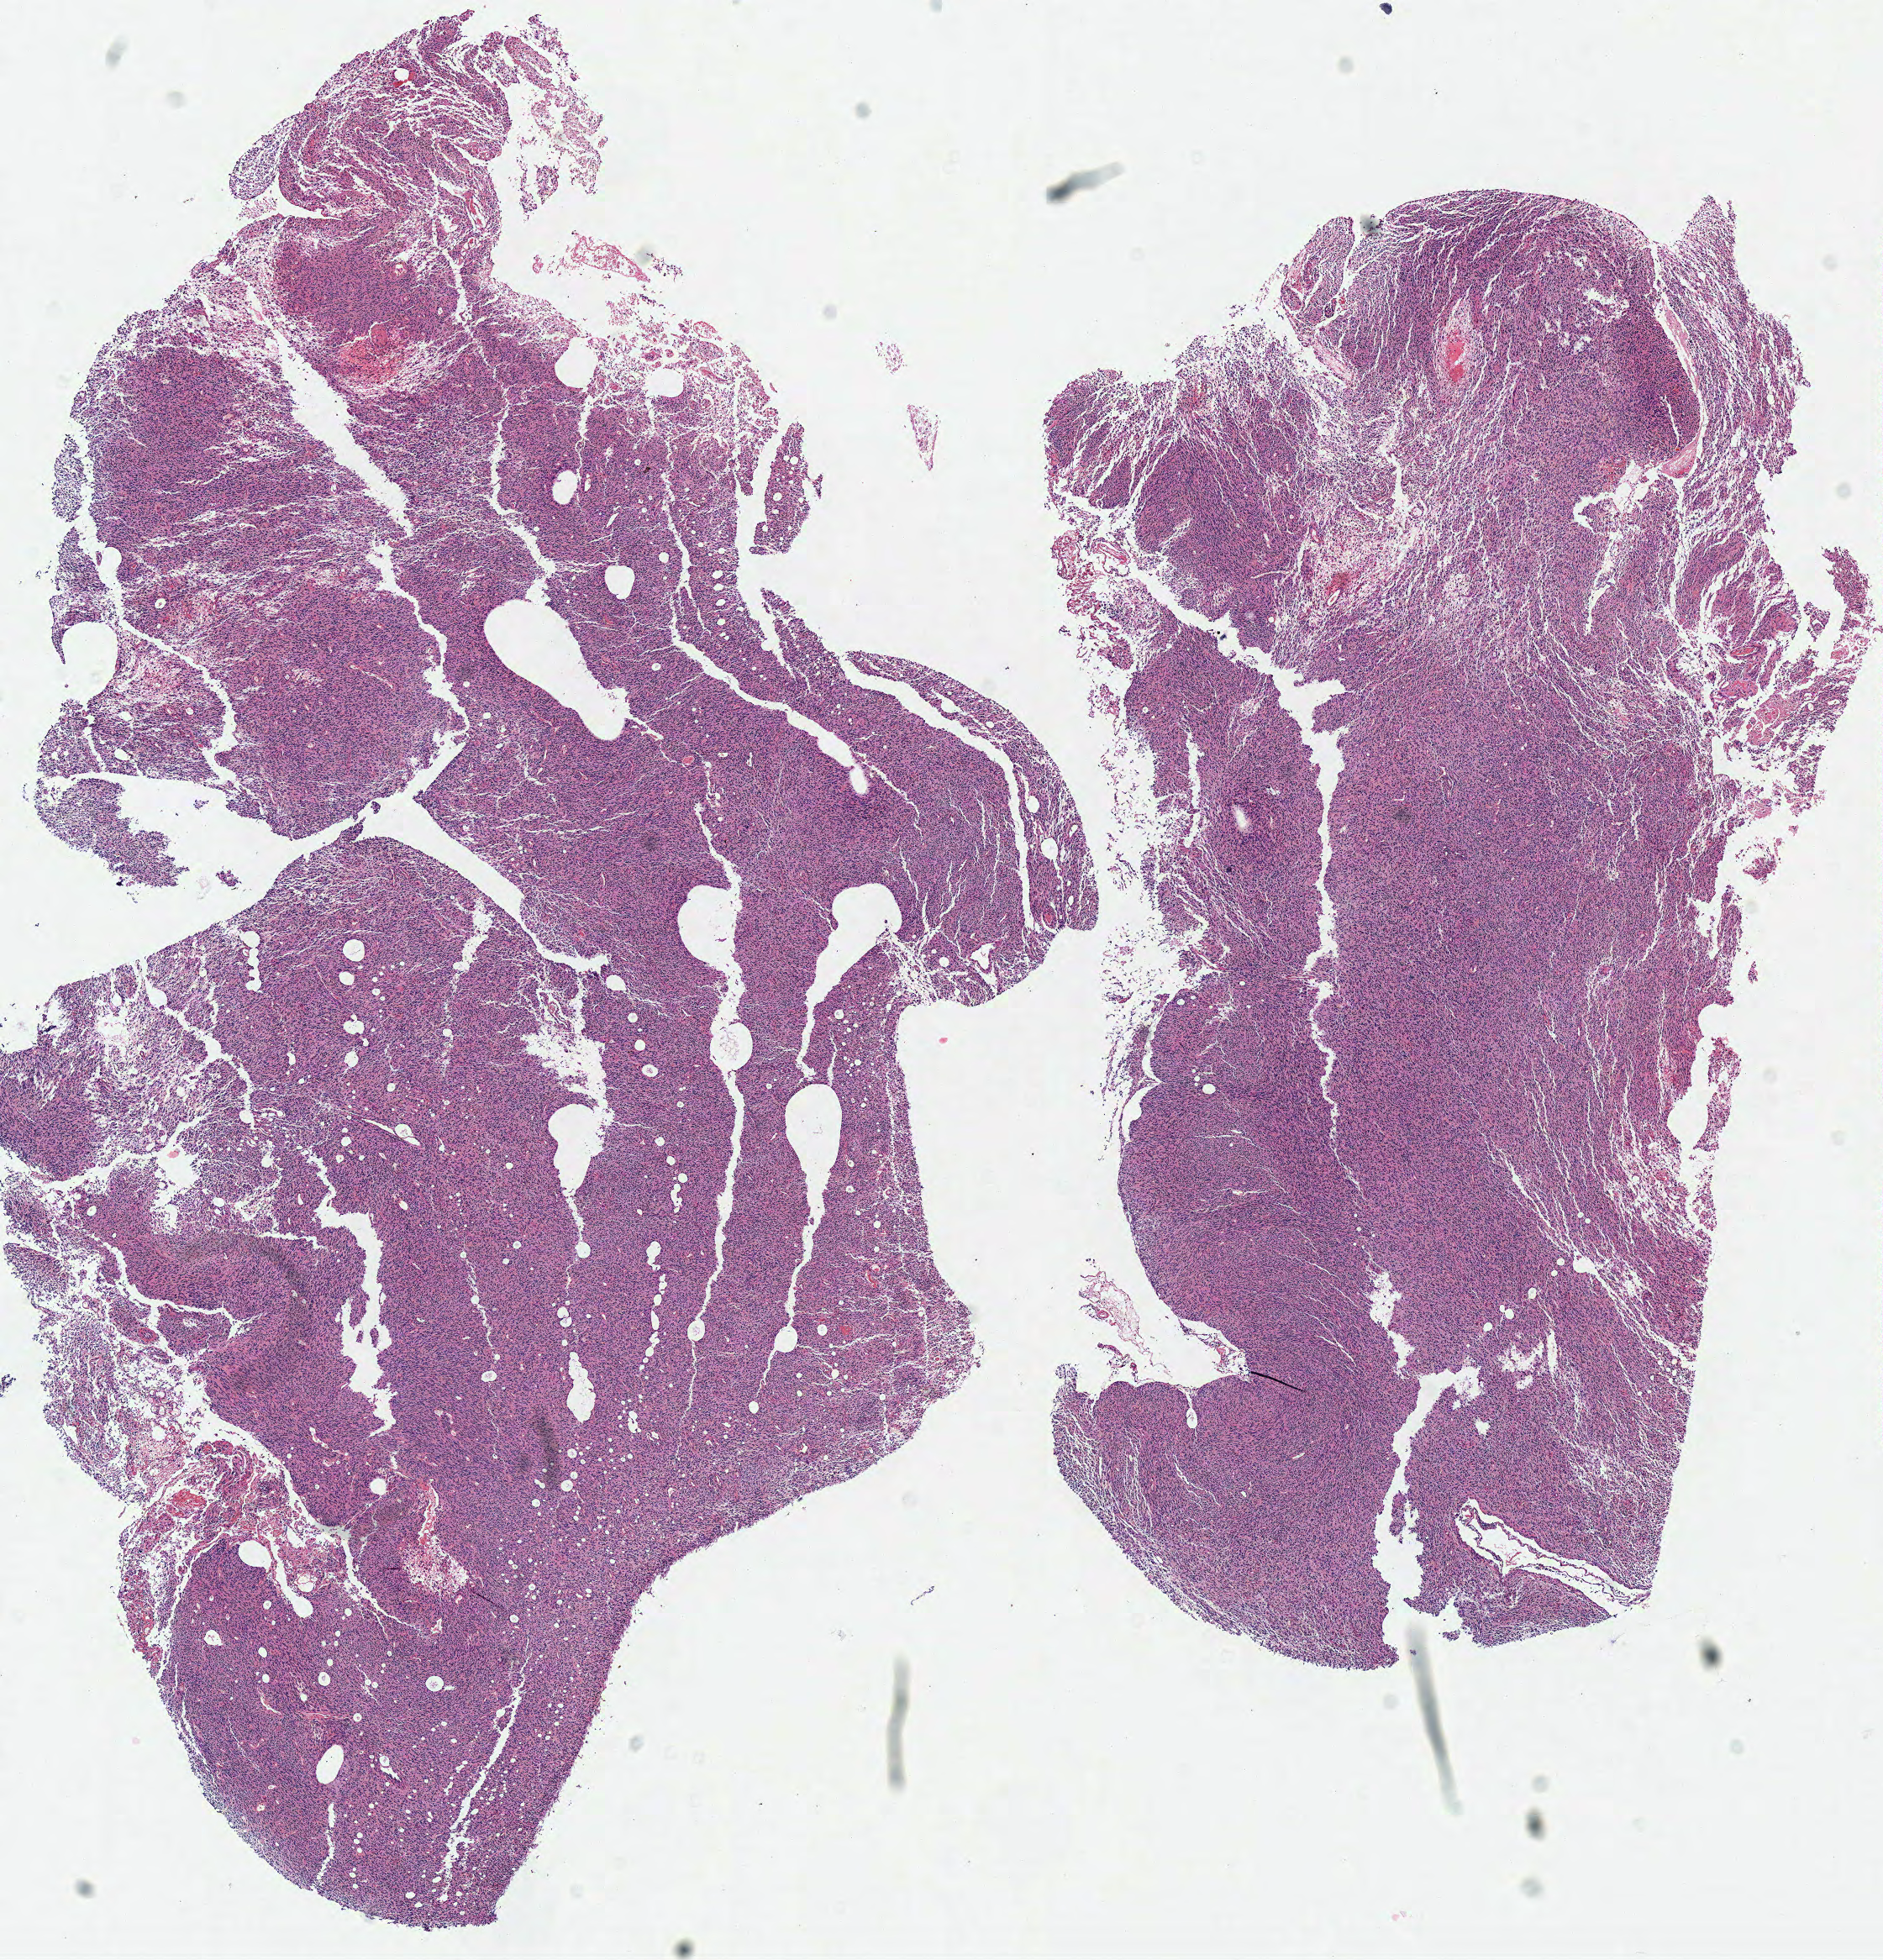
Hematoxylin and eosin (H&E) stained whole-slide image — whole scanned area (about 8.8 x 9.2 mm, slide scanned at 40x) shown as a low-resolution overview; frozen section; brain, primary tumour sample. Patient: female, age at initial diagnosis 64 years. Composition of this section per pathologist review: tumour cells 98%, tumour nuclei 85%, normal cells 0%, stromal cells 0%, necrosis 2%.
Histologic diagnosis: Glioblastoma.